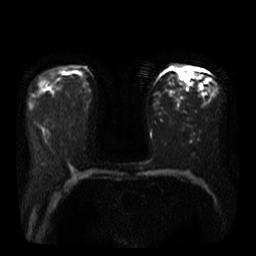
Breast MRI, one axial slice. Slice 21 of 40 in the series (ordered by position). Diffusion-weighted series; image 2 of 4 stored at this slice position (different b-values; order by instance number). 3 T. 256 × 256 image matrix, field of view 360 × 360 mm. Female patient.
Structures marked on this image (outlined manually by an expert reader):
- tumour on diffusion-weighted imaging: bounding box (x1, y1, x2, y2) in pixels: (179, 67, 191, 81)